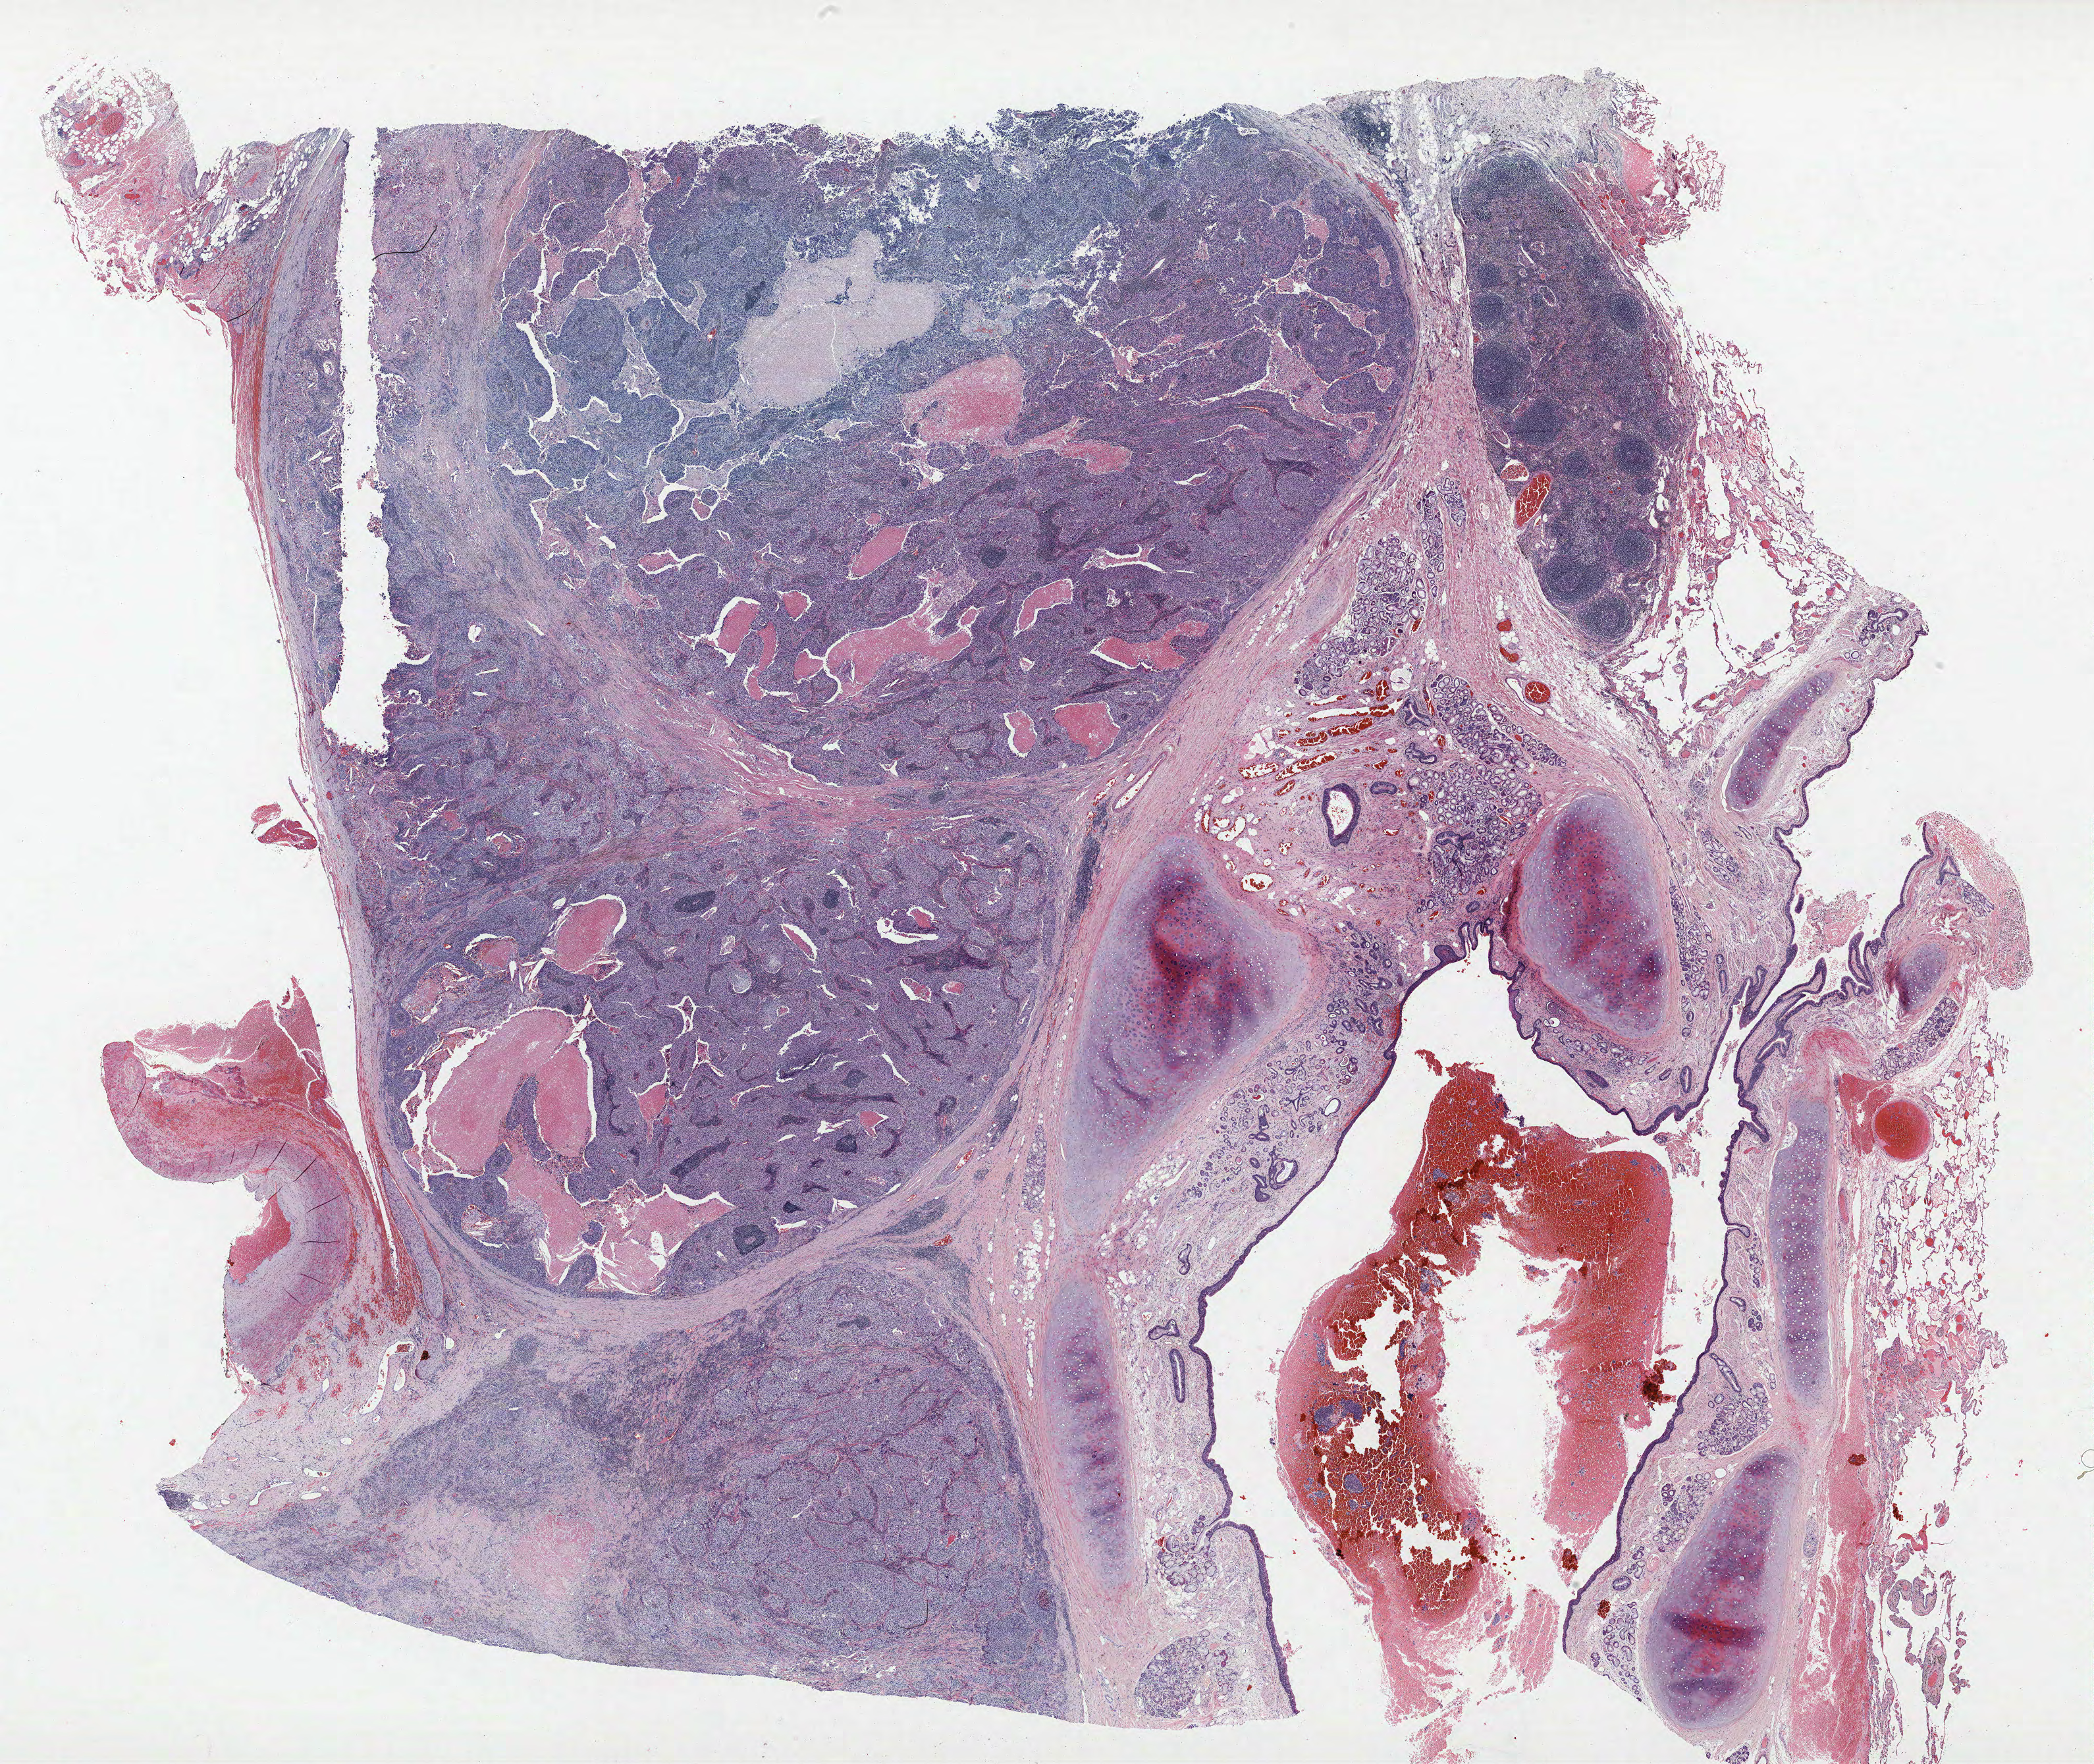
Whole-slide histology image, H&E — shown as a low-resolution overview of the whole scanned area (about 25.4 x 21.4 mm); FFPE section; lung tissue. Male, age 59 at enrolment.
Participant's lung-cancer diagnosis: Squamous cell carcinoma, NOS.